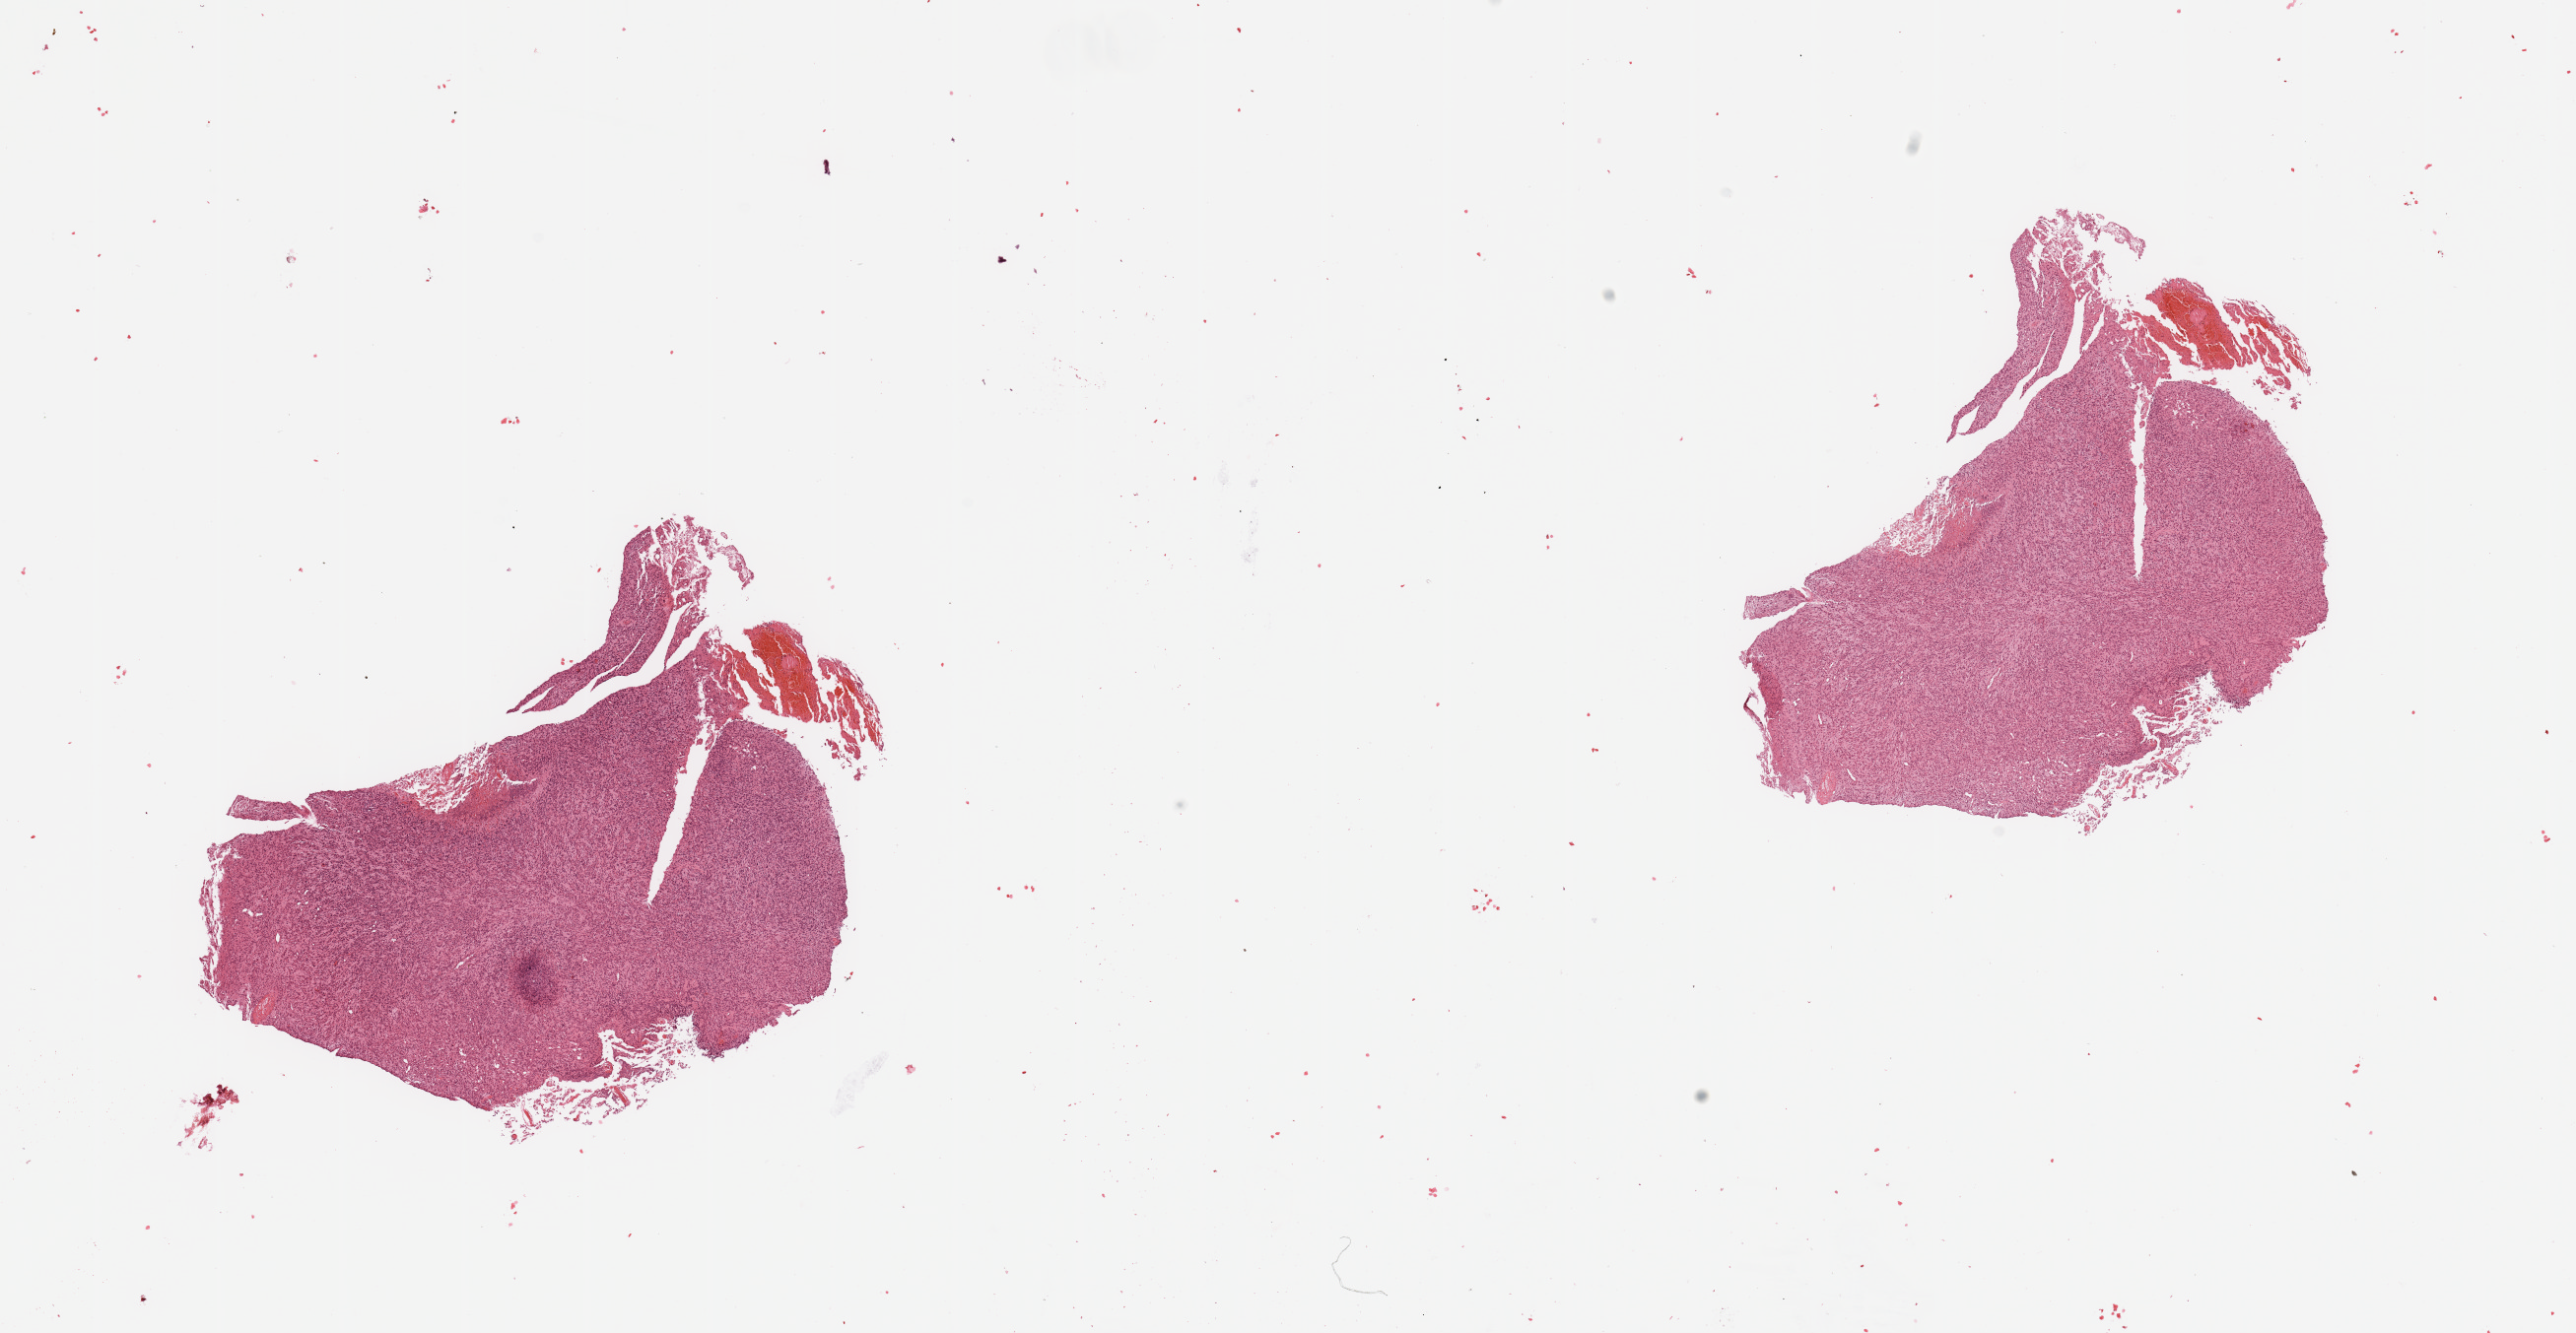
H&E whole-slide image, shown as a low-resolution overview of the whole scanned area (about 20.7 x 10.7 mm); tumour tissue sample, sampled site: brain. Male, 49 y/o. Composition of this section per pathologist review: tumour nuclei 85%, necrosis 5%.
* primary tumour site (as recorded): temporal lobe
* diagnosis: Glioblastoma